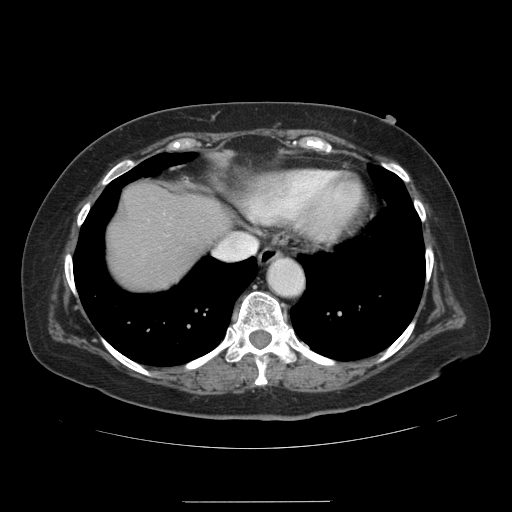
Contrast-enhanced abdominal CT, one axial slice. Slice 122 of 141 in the series (ordered by position). 120 kVp. Soft-tissue window (W 400 / L 40 HU). 2.5 mm slice thickness. 512 × 512 image matrix, field of view 393 × 393 mm. Female patient, age 74 years. From the clinical record (not read from this slice): diagnosis: colorectal cancer liver metastases, imaged before liver resection; multiple liver metastases: yes; largest metastasis: 7 cm; disease in both lobes: yes.
Annotated regions visible in this slice (outlined manually by an expert reader):
- hepatic veins: bounding box <227,233,243,240> (left, top, right, bottom; pixels)
- liver: <108,186,229,290>
- planned liver remnant (the part of the liver to remain after resection): <108,186,229,290>